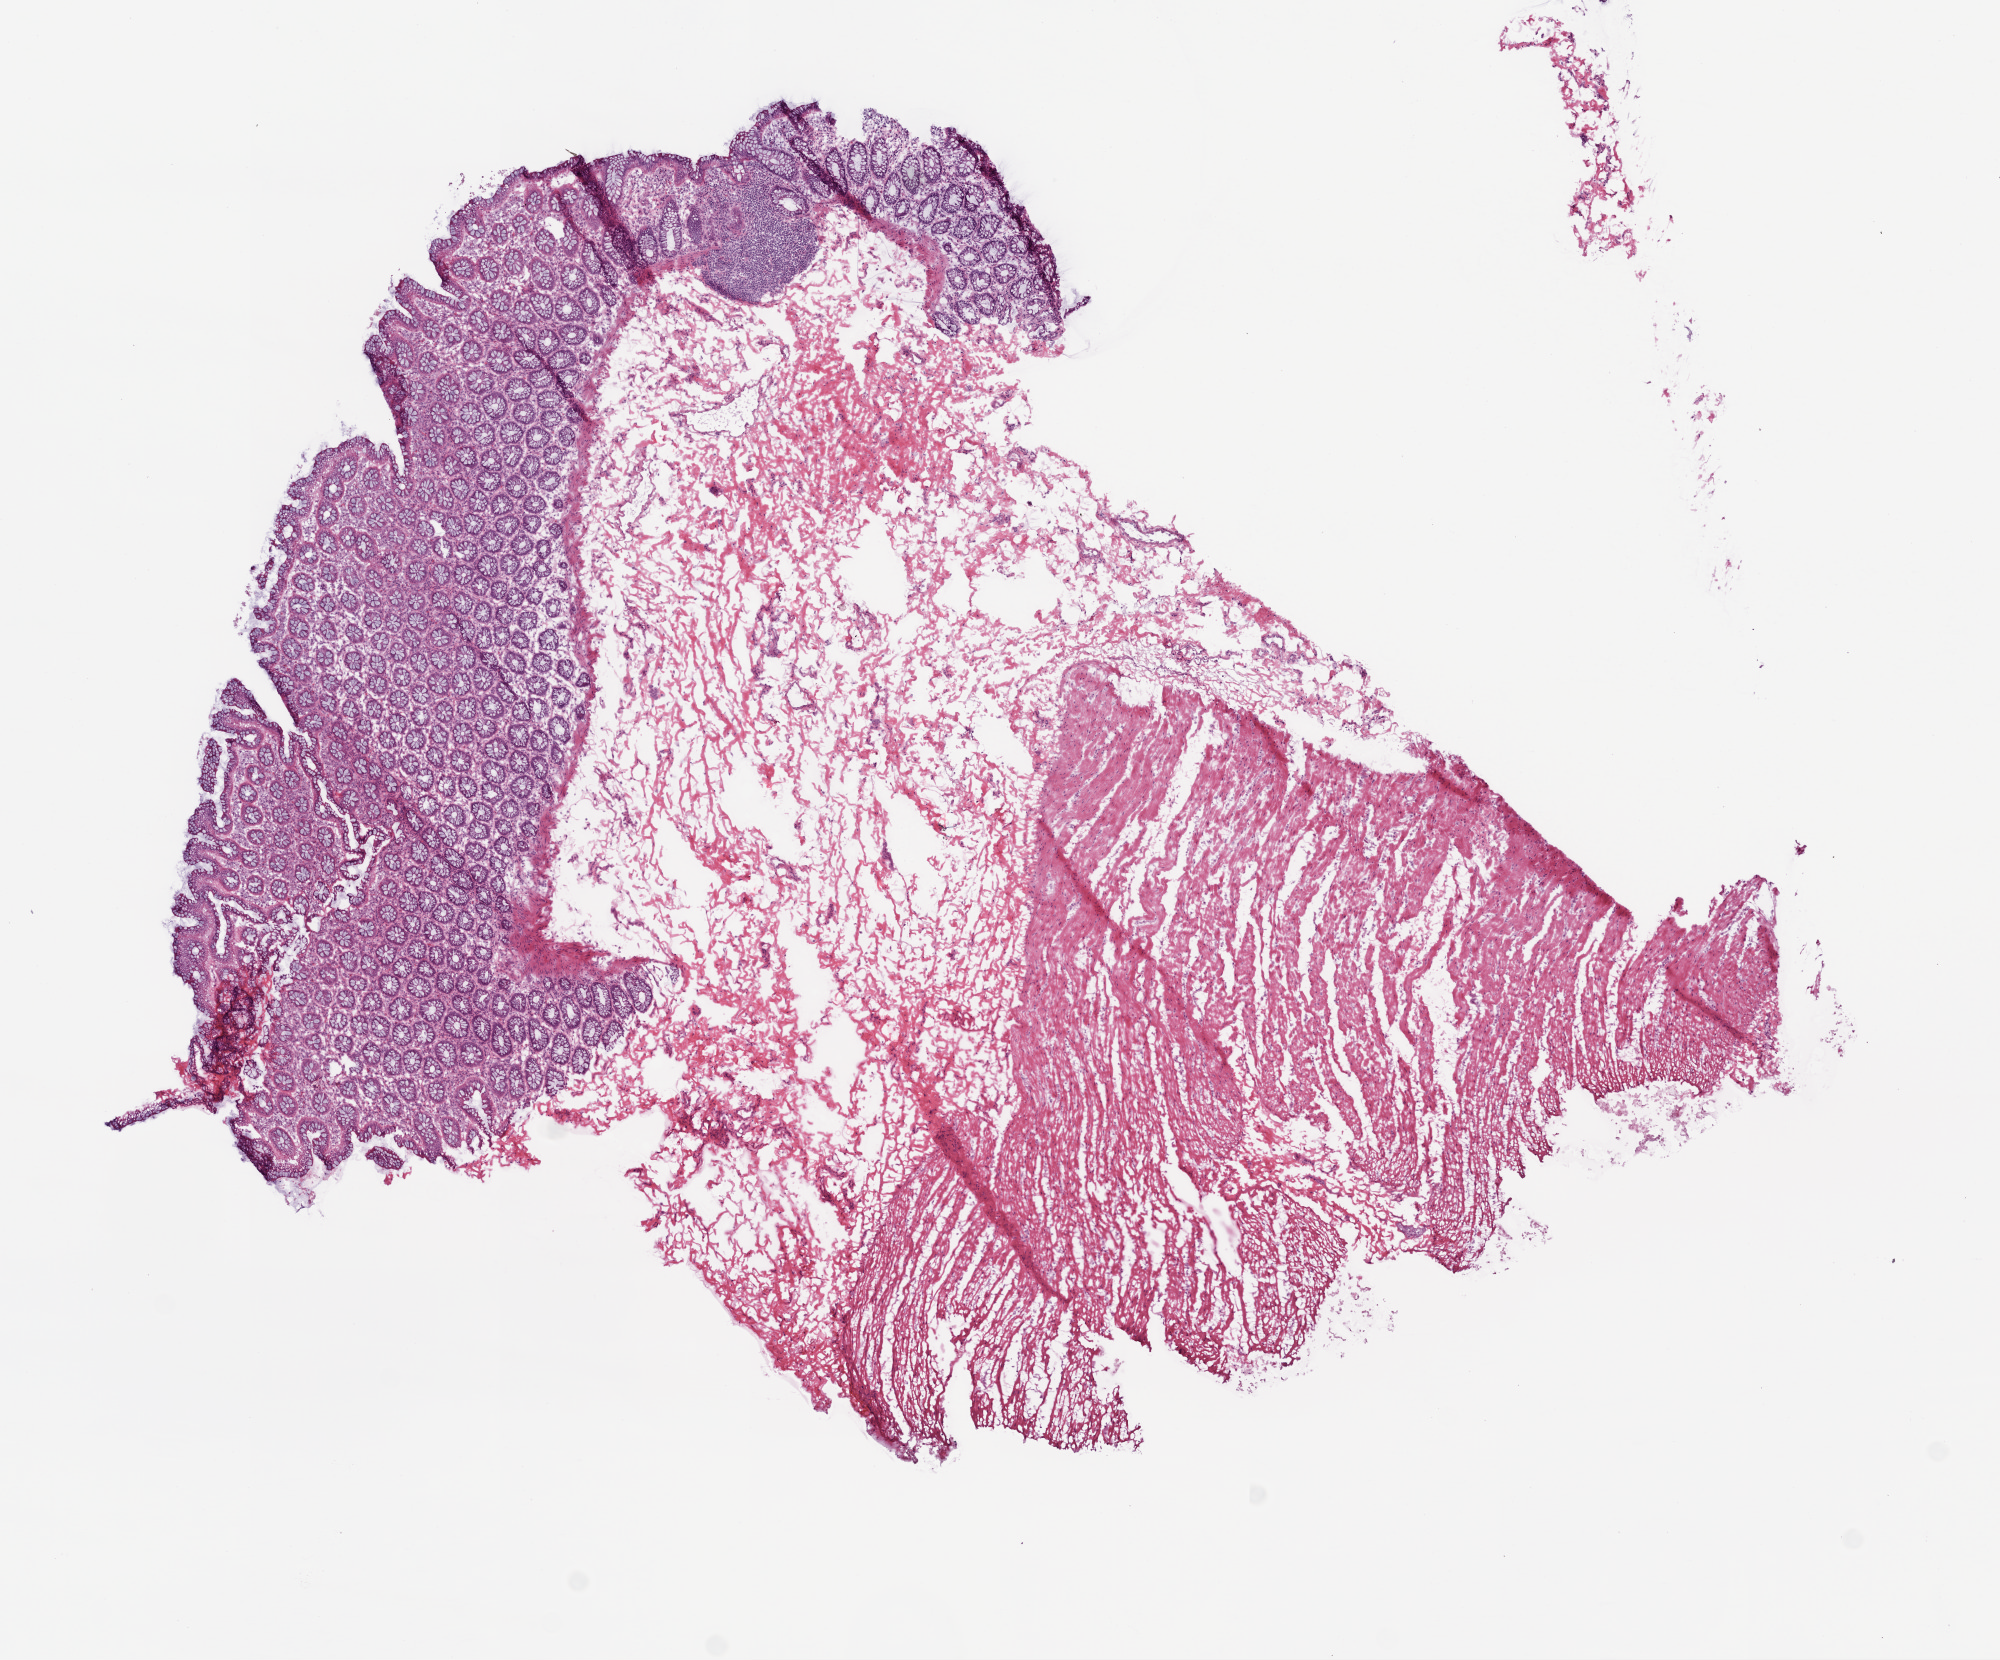
H&E-stained whole-slide image — shown as a low-resolution overview of the whole scanned area (about 8.0 x 6.7 mm). Frozen section from the top of the tissue portion. Sample: solid tissue normal (non-tumour tissue), colon. Patient: female, age at initial diagnosis 54 years.
This section: solid tissue normal sample (biorepository sample class). Patient diagnosis: Adenocarcinoma, NOS.